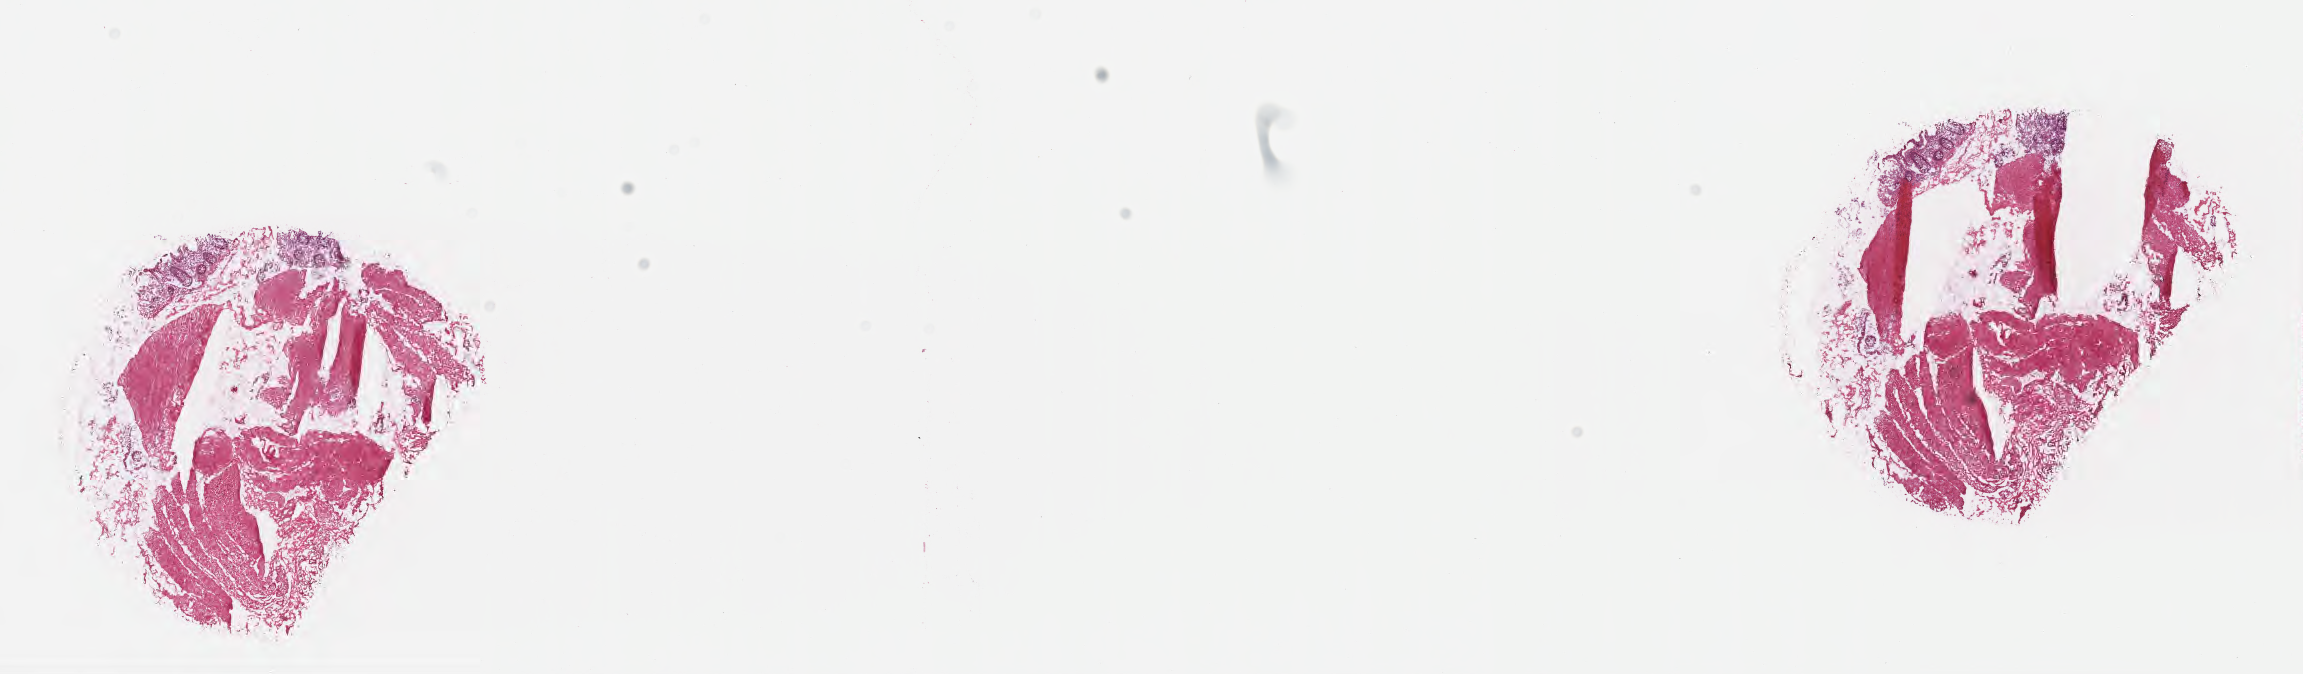
Digitized hematoxylin and eosin (H&E)-stained section — shown as a low-resolution overview of the whole scanned area (about 18.6 x 5.4 mm), frozen section, normal-tissue sample (non-tumor) from a patient with medullary carcinoma, NOS, site: splenic flexure of colon. Female, age 81 years at initial diagnosis. Pathologist review of this section (percent, as recorded): tumor cells 0%, tumor nuclei 0%, stromal cells 50%, necrosis 0%, normal cells 50%. Infiltration values recorded for this section: lymphocyte infiltration 8%, monocyte infiltration 5%, neutrophil infiltration 12%.
* this section: non-tumor tissue sample; the patient's diagnosis is given above
* section: top of the tissue portion